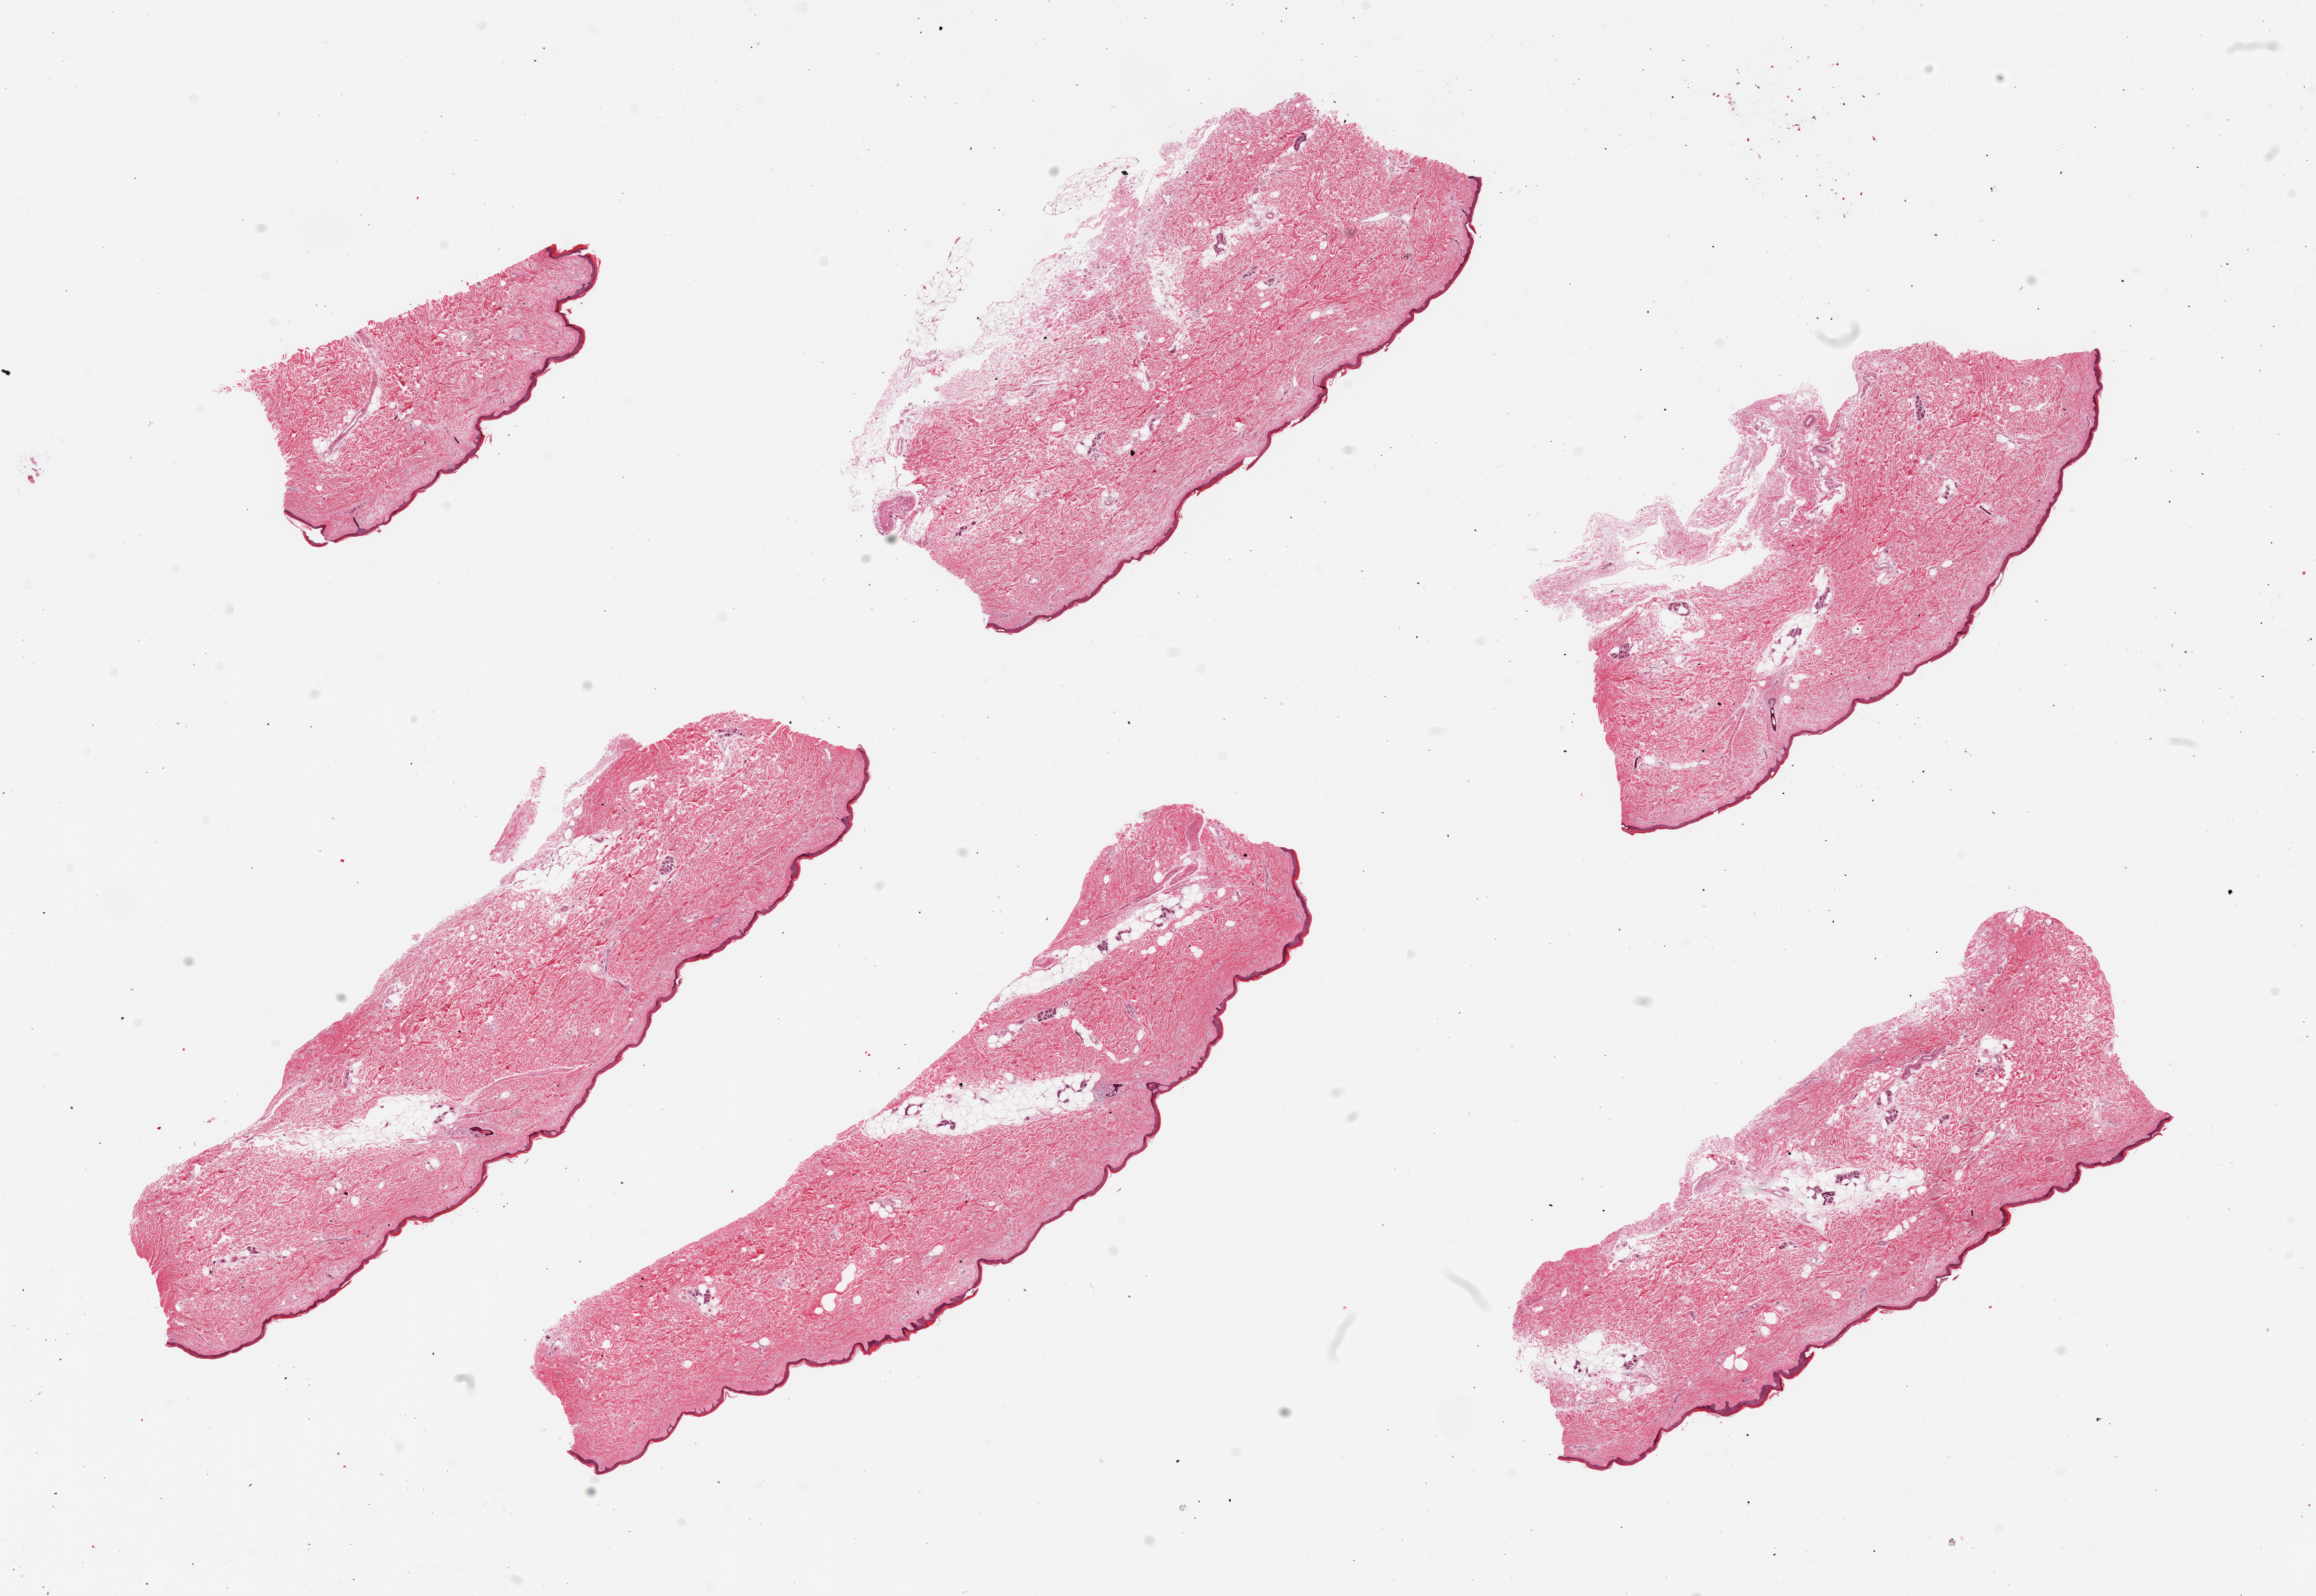
Whole-slide image, haematoxylin and eosin stain — low-resolution overview of the scanned area, about 27.6 x 19.0 mm; PAXgene-fixed, paraffin-embedded tissue; target tissue: skin of lower leg; donor tissue sample.
Reviewer comment on this tissue sample: 6 pieces; 10 - 20% internal fat; epidermis between 33 and 47um thick.